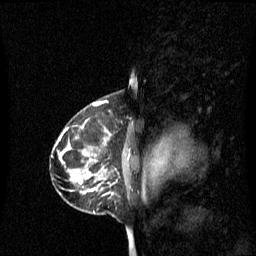
Breast MRI (dynamic contrast-enhanced), one sagittal slice; slice 44 of 60 in the series (ordered by position); dynamic contrast-enhanced series, image 2 of 3 at this slice position (ordered by acquisition); 1.5 T; TE 4.2 ms, TR 8.4 ms; 2.1 mm slice thickness; 256 × 256 image matrix, field of view 240 × 240 mm. Patient: female, 42 years. Case-level facts recorded for this patient, not image findings: setting: breast cancer imaged before/during neoadjuvant chemotherapy; receptor status: HR-positive, HER2-negative.
Structures marked on this image (semi-automatic segmentation, software-assisted and operator-edited):
- analysis volume of interest (the breast-tissue region the enhancement analysis was run in; not a lesion): box from (x=68, y=108) to (x=137, y=195) px
- tumour enhancement mask (voxels above the 70 % enhancement threshold inside the analysis volume of interest): (x=80, y=182)–(x=97, y=191)